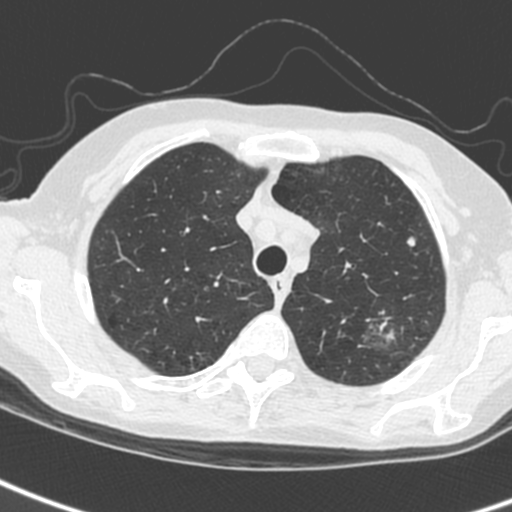
Chest CT (low-dose screening protocol), one axial image. First (baseline) screen. Lung window (W 1500 / L -600 HU). 512 × 512 image matrix, field of view 284 × 284 mm. Female participant, aged 61 years at enrolment.
2 lesions marked by an expert reader on this slice (largest first), bounding box <353,306,412,352> (left, top, right, bottom; pixels); <395,226,430,256>. The screening reader recorded 2 non-calcified nodules or masses ≥4 mm on this exam; which of them these boxes mark is not recorded. Official screen result: positive, change unspecified: nodule(s) >= 4 mm or enlarging nodule(s), mass(es), or other non-specific abnormalities suspicious for lung cancer. Participant outcome: lung cancer diagnosed 29 days after this screen — small cell carcinoma, NOS, left upper lobe, stage IV (AJCC 6th edition).